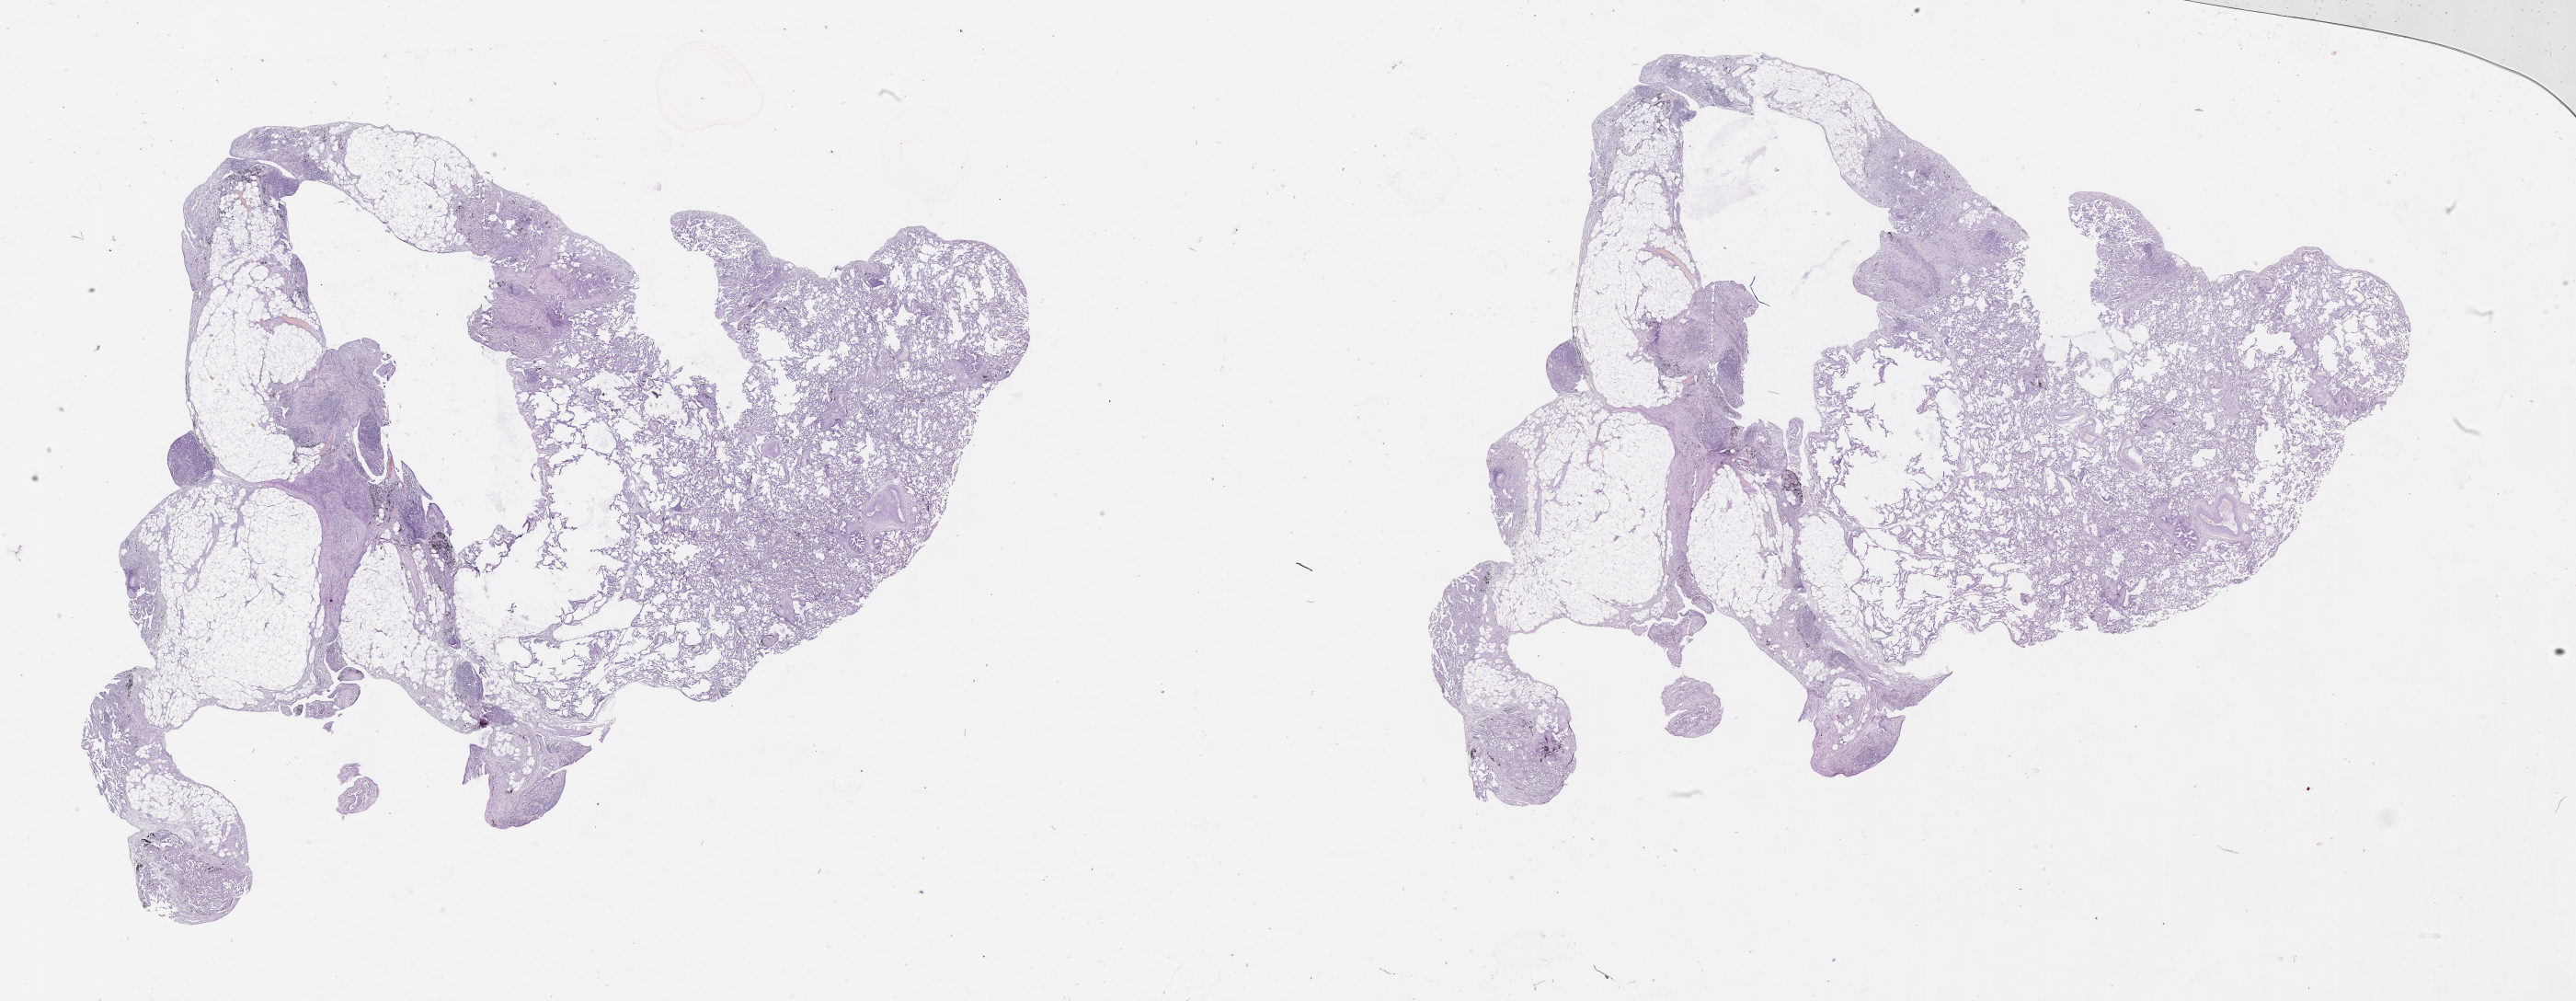
Whole-slide histology image, H&E-stained, a low-resolution overview of the entire scanned area, about 45.1 x 17.5 mm (from a 20x scan), lung, normal (non-tumour) tissue. Patient: male, age 70 years.
* this section: normal (non-tumour) tissue from the same patient
* patient diagnosis (cohort enrolment): squamous cell carcinoma (lung)